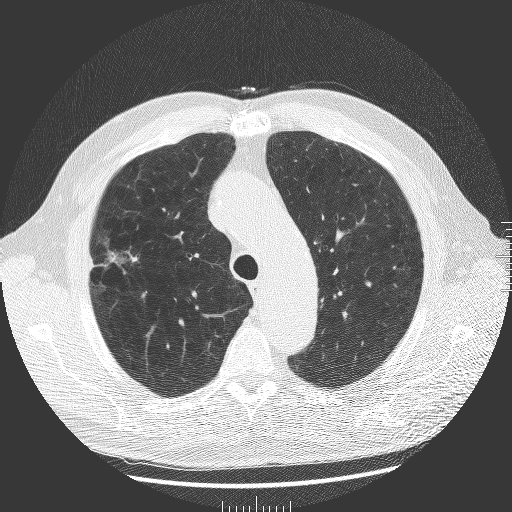
Low-dose screening chest CT, one axial slice. Slice 142 of 181 in the series (ordered by position). 120 kVp. Lung window (W 1500 / L -600 HU). 512 × 512 image matrix, field of view 380 × 380 mm.
Outlined on this slice (manually delineated by an expert):
- lesion 1 (tumor, upper lobe of right lung): bounding box <108,251,135,263> (left, top, right, bottom; pixels)